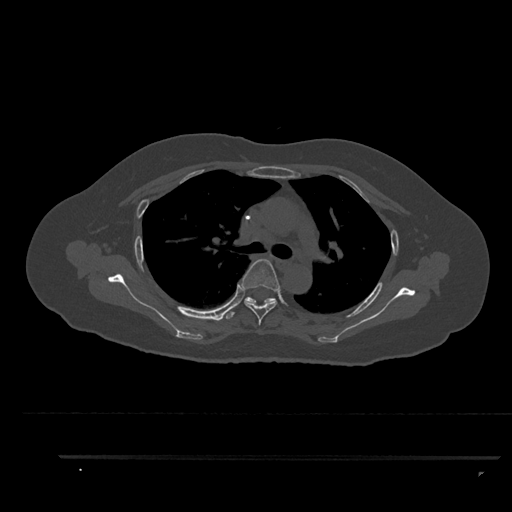
CT including the spine, one axial slice; slice 630 of 797 in the series (ordered by position); reconstruction kernel Br40s/3; 120 kVp; bone window (W 1800 / L 400 HU); 512 × 512 image matrix. Patient: female, 44 years. Case-level facts recorded for this patient, not image findings: primary cancer: renal; vertebrae with lytic lesions (as recorded): L1.
Outlined on this slice (semi-automatically segmented with operator editing):
- T4 vertebra: bounding box [x1, y1, x2, y2] px = [240, 259, 280, 326]
- T5 vertebra: [226, 297, 275, 319]